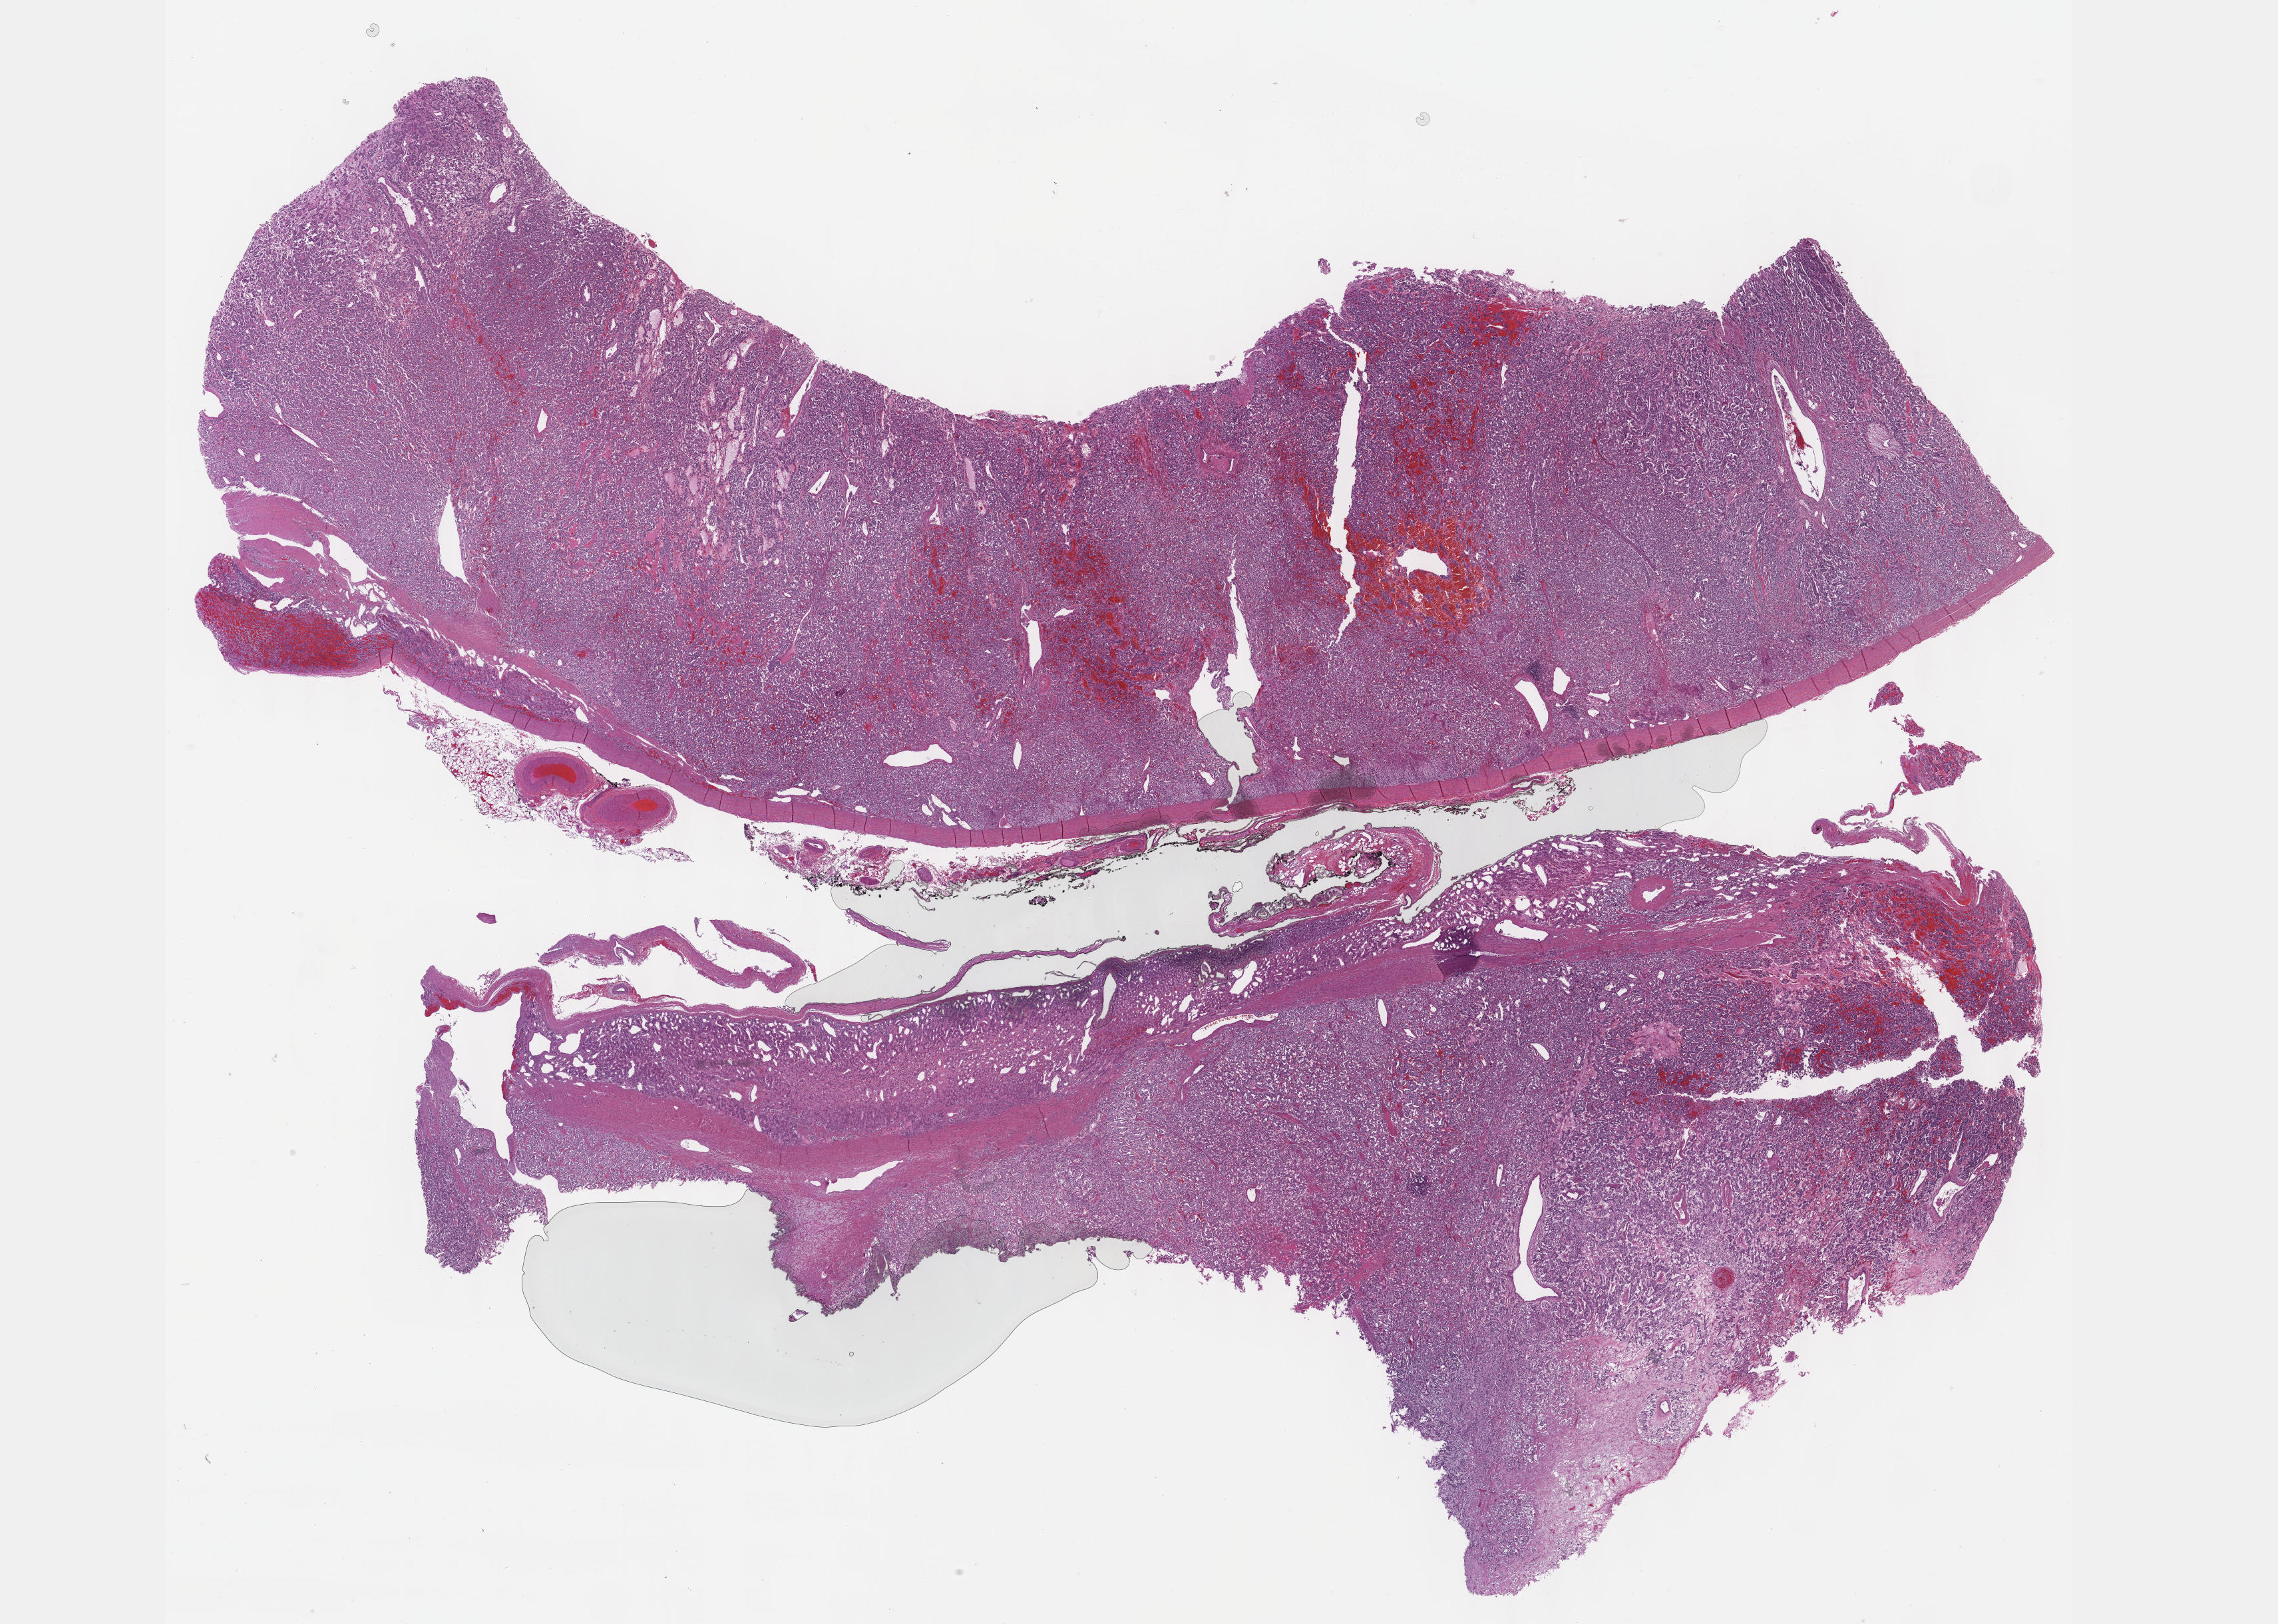
Digitized Hematoxylin and eosin (H&E) stained tissue section (whole slide), whole scanned area (about 27.7 x 19.7 mm) shown as a low-resolution overview. Formalin-fixed paraffin-embedded (FFPE) diagnostic section. Primary tumour sample from the adrenal gland. Male patient; age at initial diagnosis 23 years.
Laterality: right. Diagnosis: Pheochromocytoma, NOS.